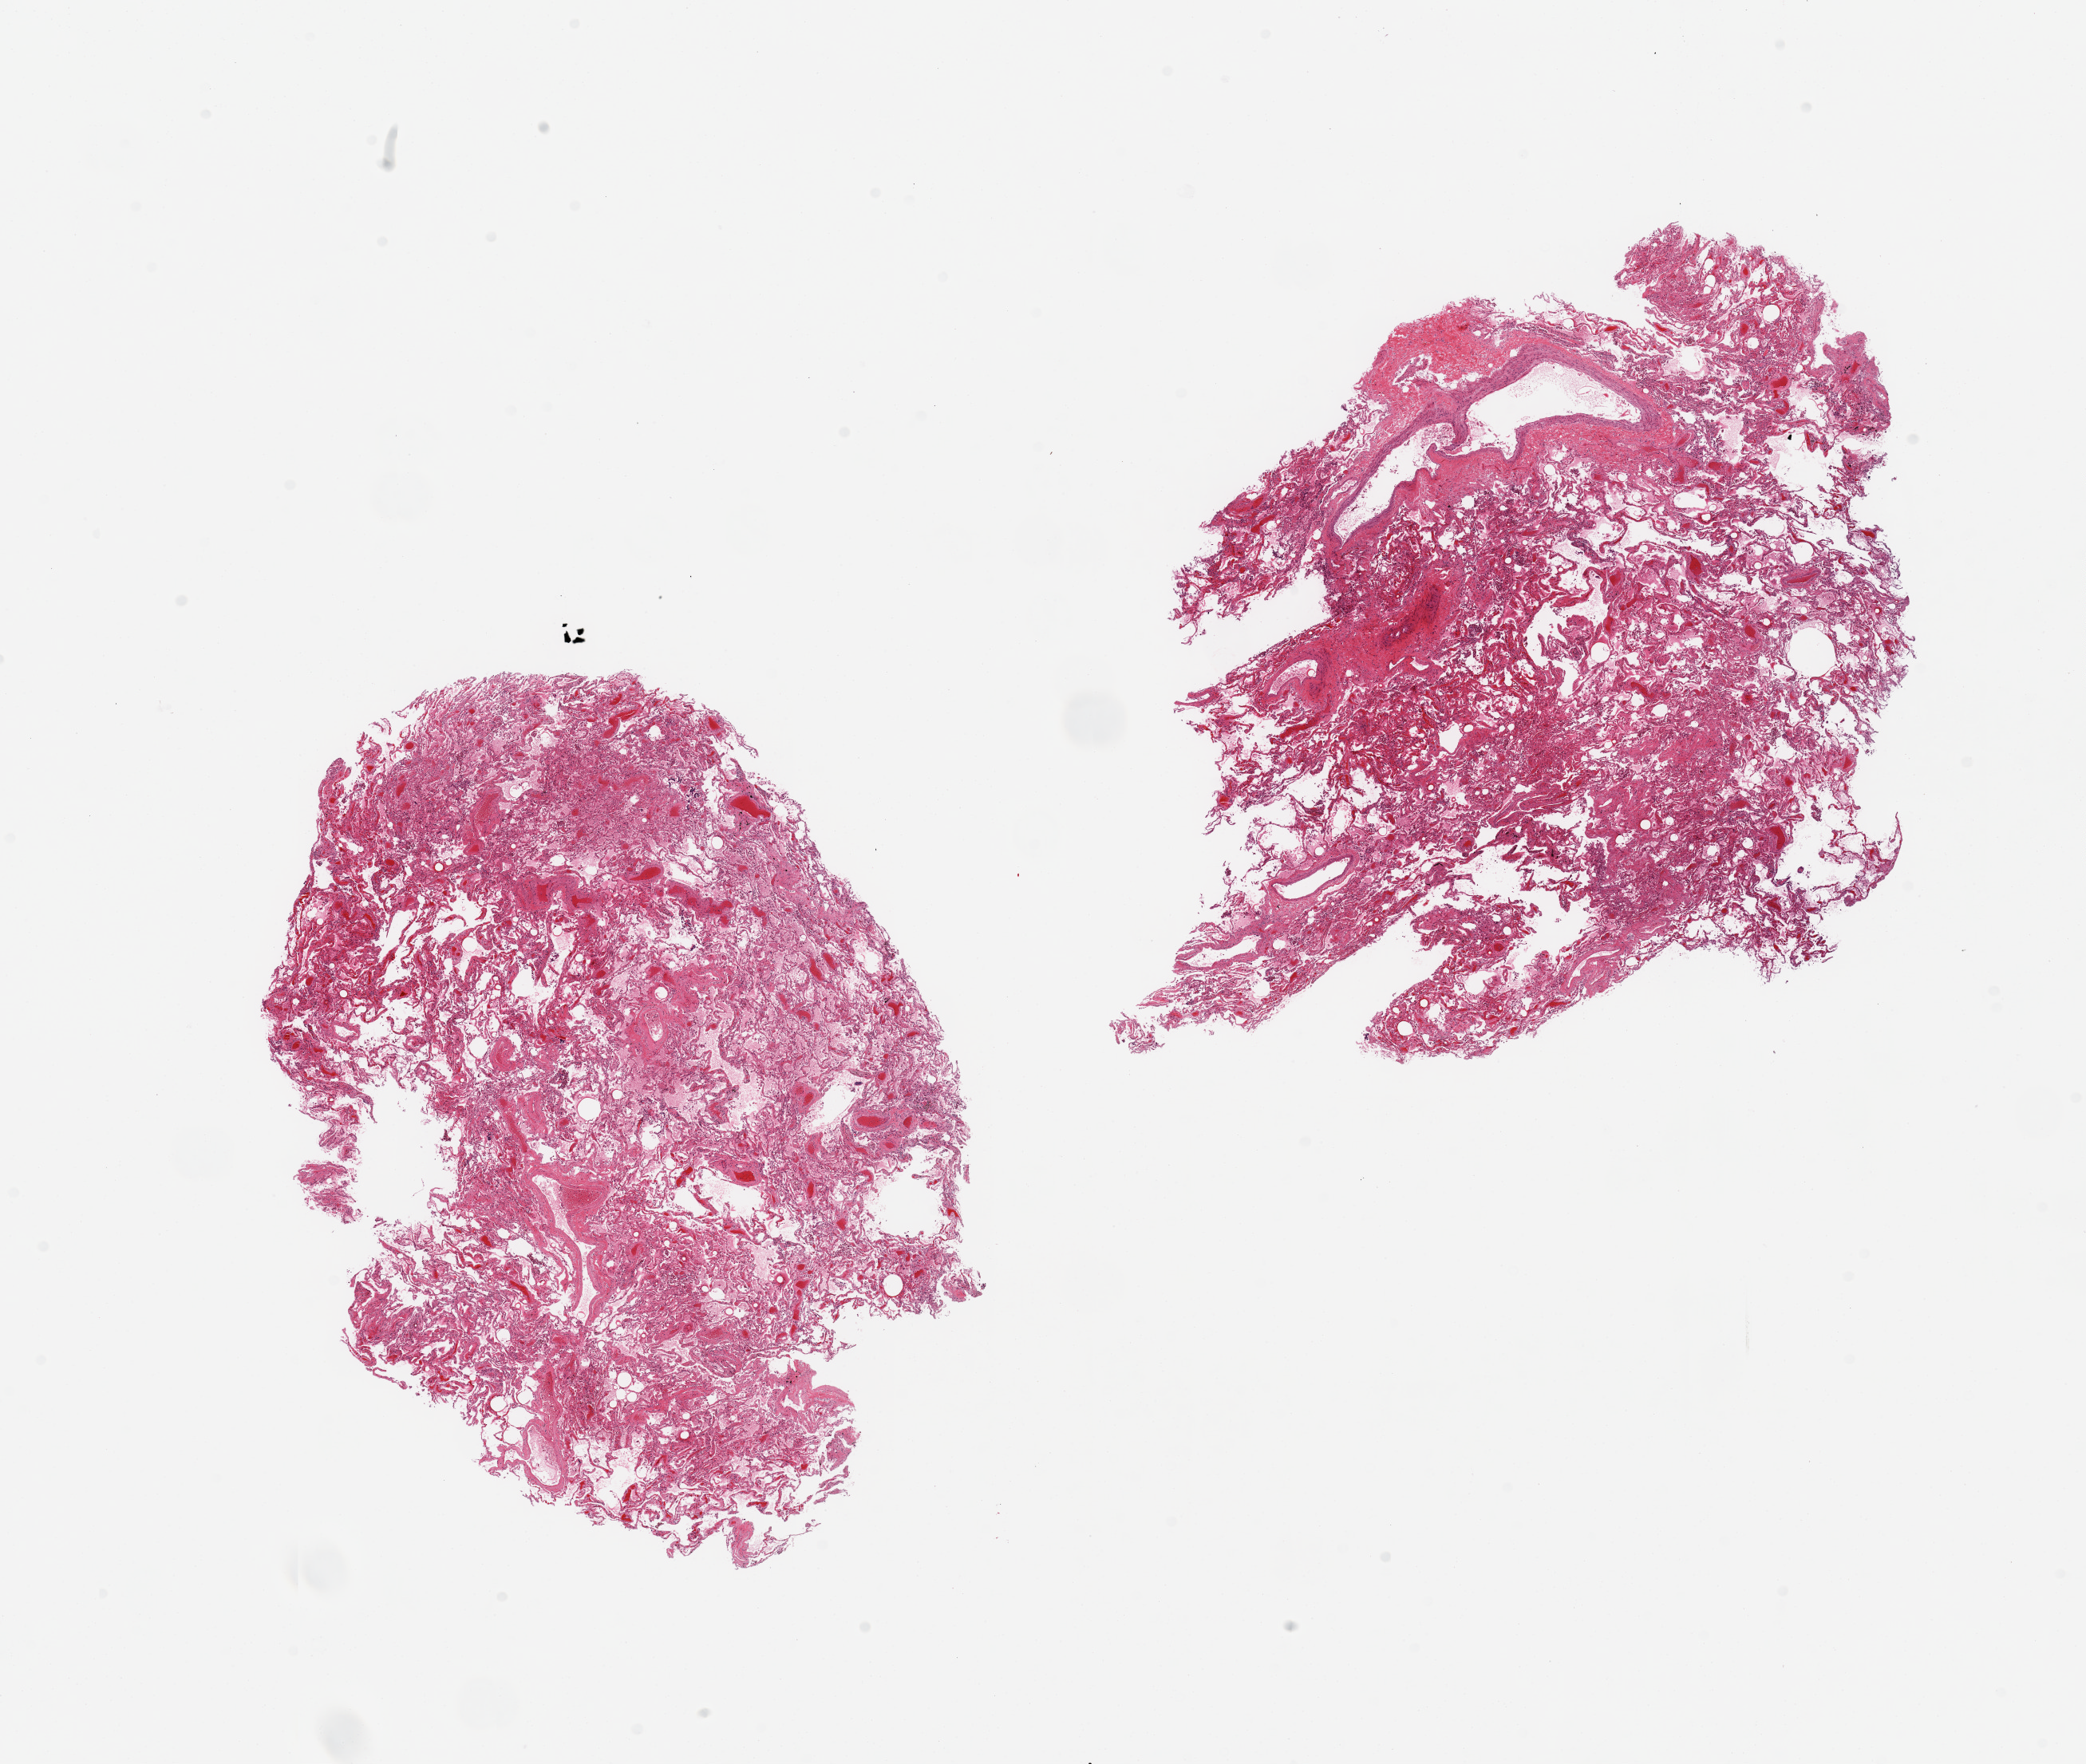
Whole-slide image, haematoxylin and eosin stain, shown as a low-resolution overview of the whole scanned area (about 20.7 x 17.5 mm). PAXgene-fixed paraffin-embedded (PFPE) section. Sampled site (target tissue): lung. Tissue donor sample. Donor sex: male.
Pathologist's review note for this sample: 2 pieces; congestion, numerous macrophages, includes several large vessels.